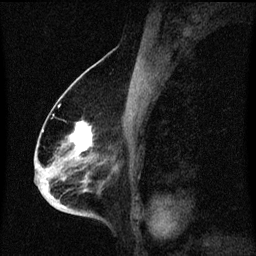
Breast MRI (dynamic contrast-enhanced), one sagittal slice. Position 36 of 60 along the scan axis. Dynamic contrast-enhanced series, image 2 of 3 at this slice position (ordered by acquisition). 1.5 T. TE 4.2 ms, TR 8.4 ms. 2 mm slice thickness. 256 × 256 image matrix, field of view 200 × 200 mm. Female patient, age 68 years. Case-level facts recorded for this patient, not image findings: setting: breast cancer imaged before/during neoadjuvant chemotherapy; receptor status: triple-negative.
Structures marked on this image (semi-automatic segmentation, software-assisted and operator-edited):
- analysis volume of interest (the breast-tissue region the enhancement analysis was run in; not a lesion): box from (x=36, y=96) to (x=113, y=213) px
- tumour enhancement mask (voxels above the 70 % enhancement threshold inside the analysis volume of interest): (x=69, y=122)–(x=92, y=191)